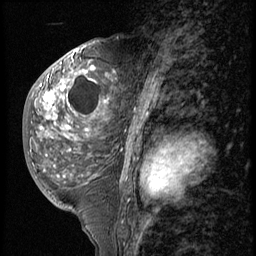
Breast MRI (dynamic contrast-enhanced), one sagittal slice. 3 images stored at this slice position (order not interpretable as contrast timing). 1.5 T. TE 4.2 ms, TR 9 ms. 2.5 mm slice thickness. 256 × 256 image matrix, field of view 180 × 180 mm. Patient: female, 50 years. Case-level facts recorded for this patient, not image findings: setting: breast cancer imaged before/during neoadjuvant chemotherapy; receptor status: triple-negative.
Annotated regions visible in this slice (semi-automatic segmentation, software-assisted and operator-edited):
- analysis volume of interest (the breast-tissue region the enhancement analysis was run in; not a lesion): bounding box (x1, y1, x2, y2) in pixels: (25, 50, 118, 191)
- tumour enhancement mask (voxels above the 140 % enhancement threshold inside the analysis volume of interest): (44, 68, 108, 104)